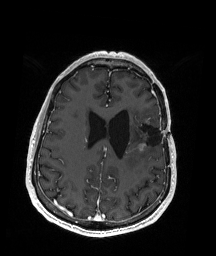
Brain MRI from a brain-tumour surgery series, one axial slice; position 69 of 192 along the scan axis; T1-weighted post-contrast; 1 mm slice thickness; 216 × 256 image matrix, field of view 211 × 250 mm. From the clinical record (not read from this slice): histopathology: Oligodendroglioma; WHO grade: 2; IDH mutation: yes; tumour location: Left Insular.
Annotated regions visible in this slice (outlined manually by an expert reader):
- previous resection cavity: box from (x=132, y=121) to (x=163, y=146) px
- tumour: (x=138, y=117)–(x=152, y=152)